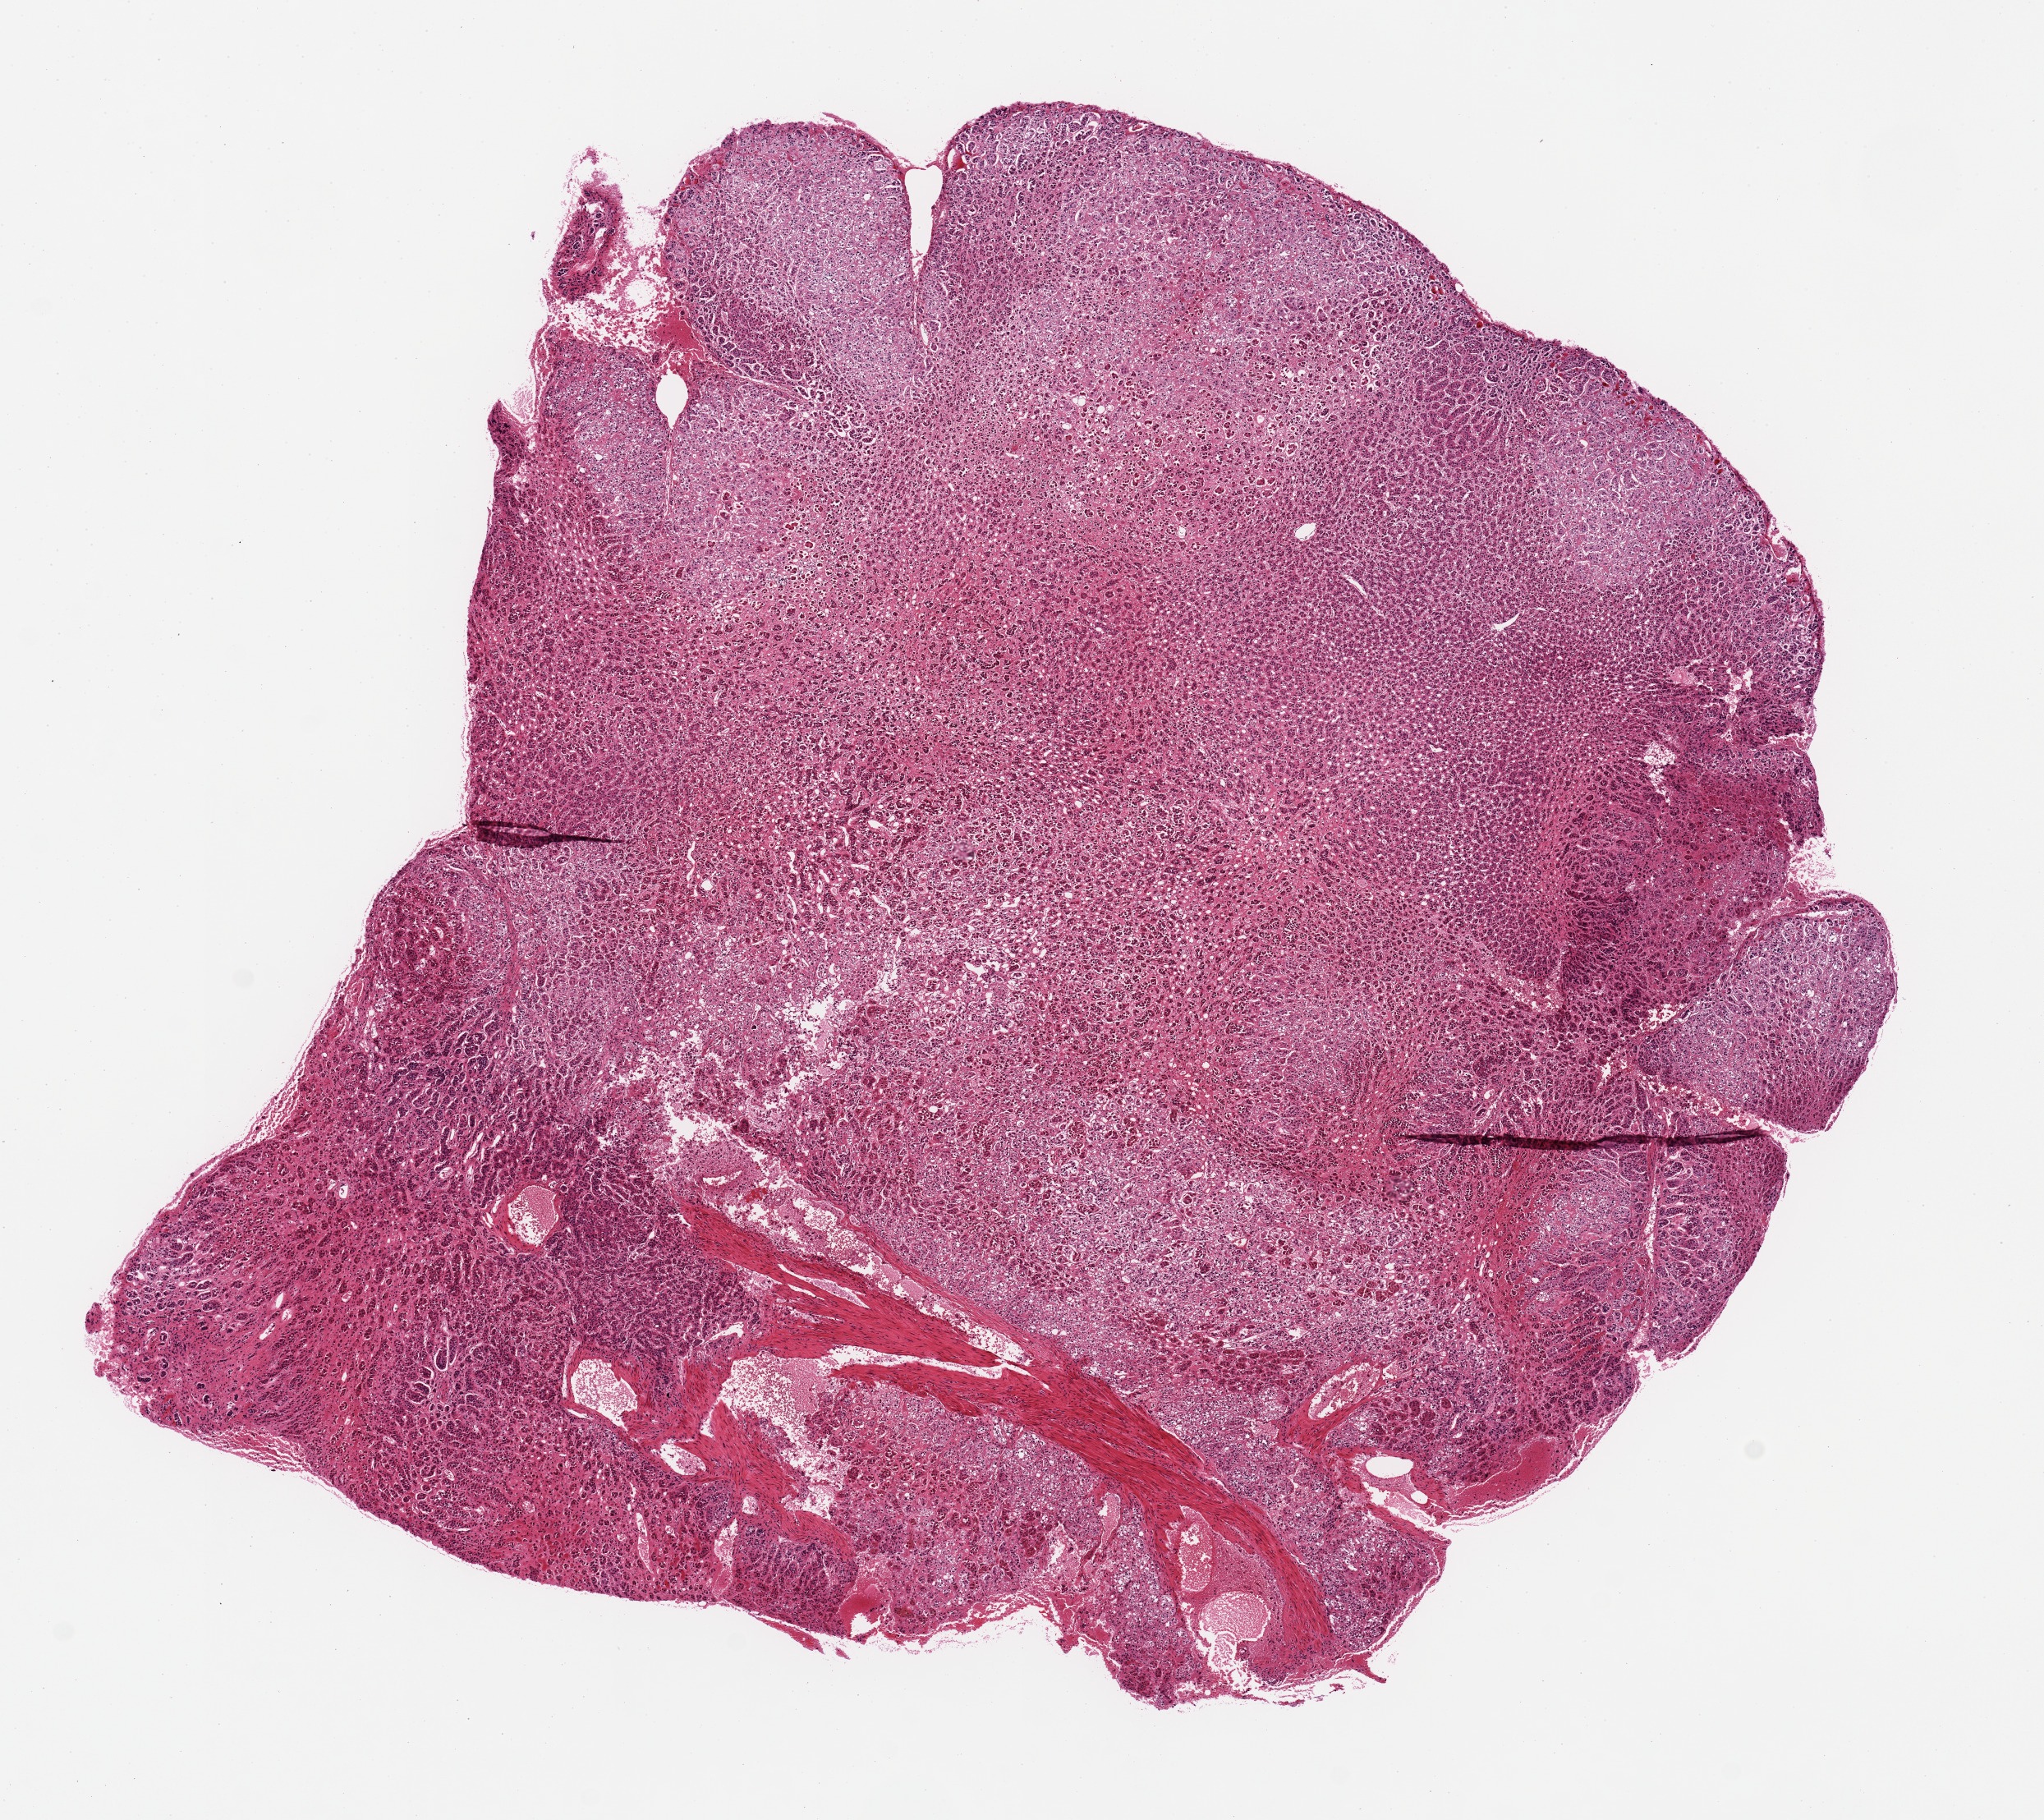
Whole-slide image, H&E stain — low-resolution overview of the scanned area, about 9.8 x 8.8 mm (acquisition: 20x scan); PAXgene-fixed paraffin-embedded (PFPE) section; target tissue: adrenal gland; donor tissue sample.
Review note (as recorded): 8x7mm. All cortex, no fat.